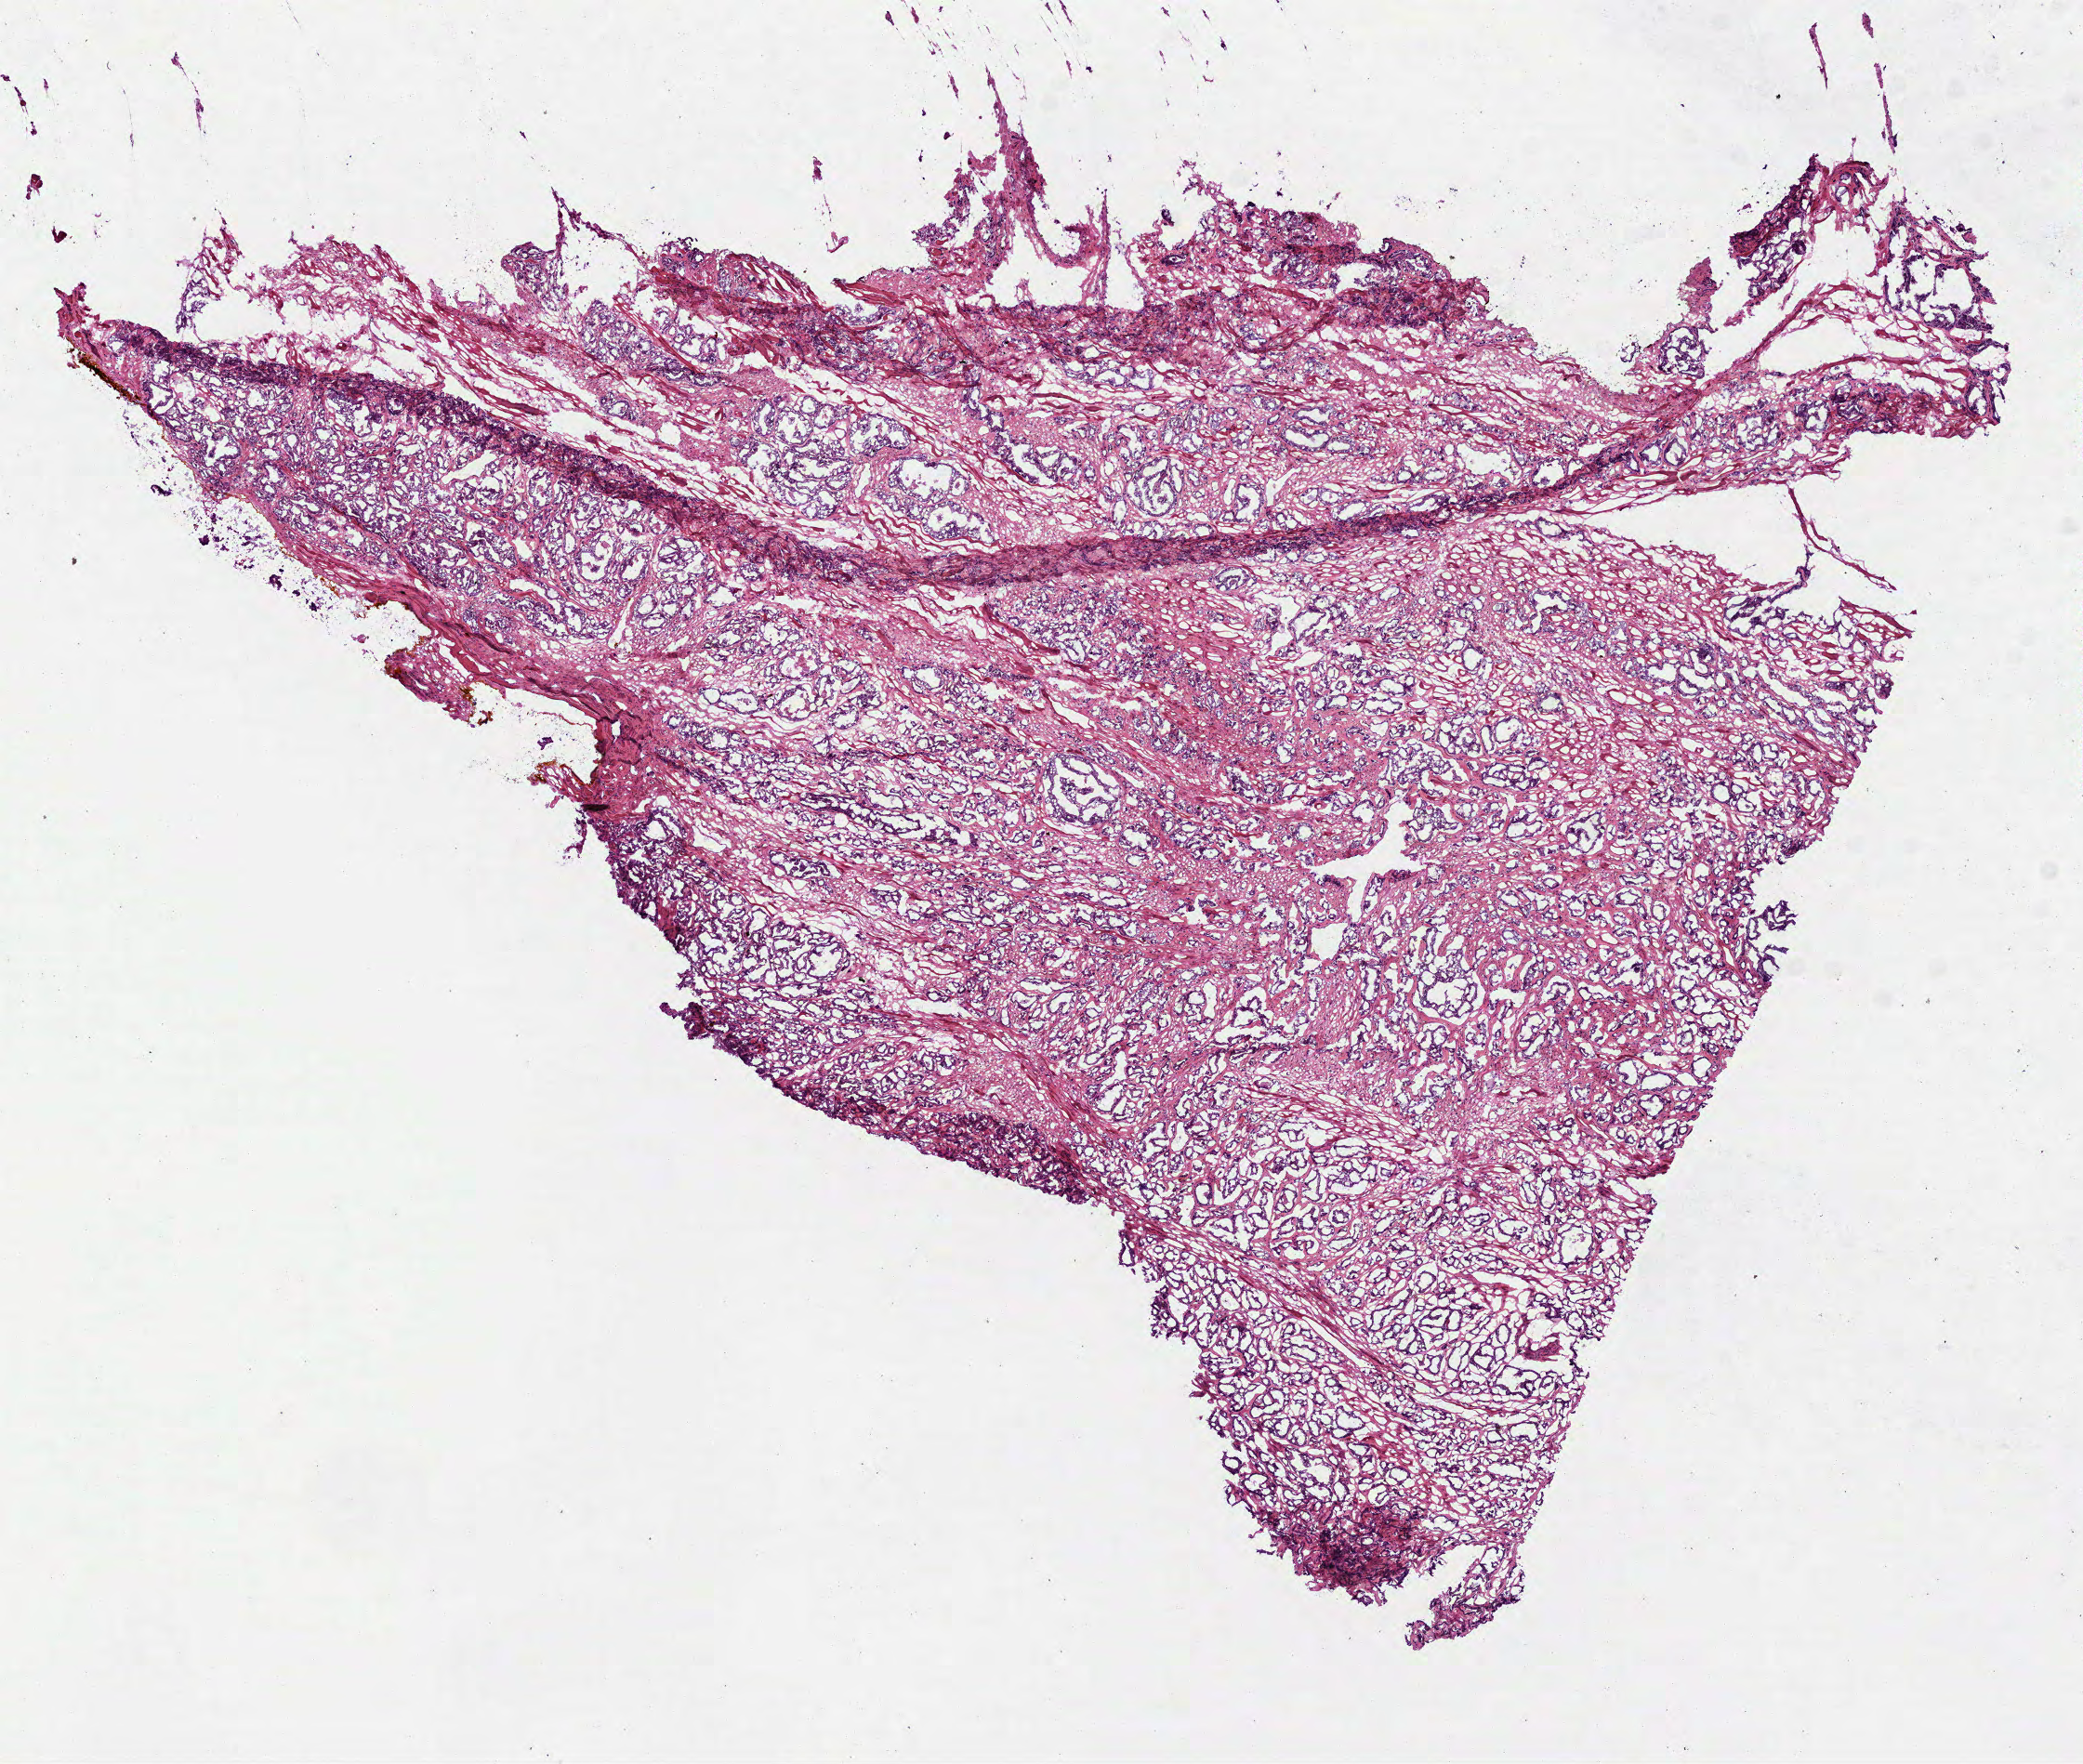
Whole-slide histology image, Hematoxylin and eosin (H&E) stained, a low-resolution overview of the entire scanned area, about 9.0 x 7.7 mm (acquisition: 40x scan). Frozen section from the bottom of the tissue portion. Sample: primary tumour, prostate. Patient: male, age at initial diagnosis 61 years. Gleason score: 7 (4+3). Slide review estimates, as recorded: tumour cells 65%, tumour nuclei 65%, normal cells 15%, stromal cells 20%, necrosis 0%. Inflammatory infiltration, as recorded: lymphocyte infiltration 2%, monocyte infiltration 0%, neutrophil infiltration 0%.
- pathologic diagnosis: Acinar cell carcinoma (prostate gland)